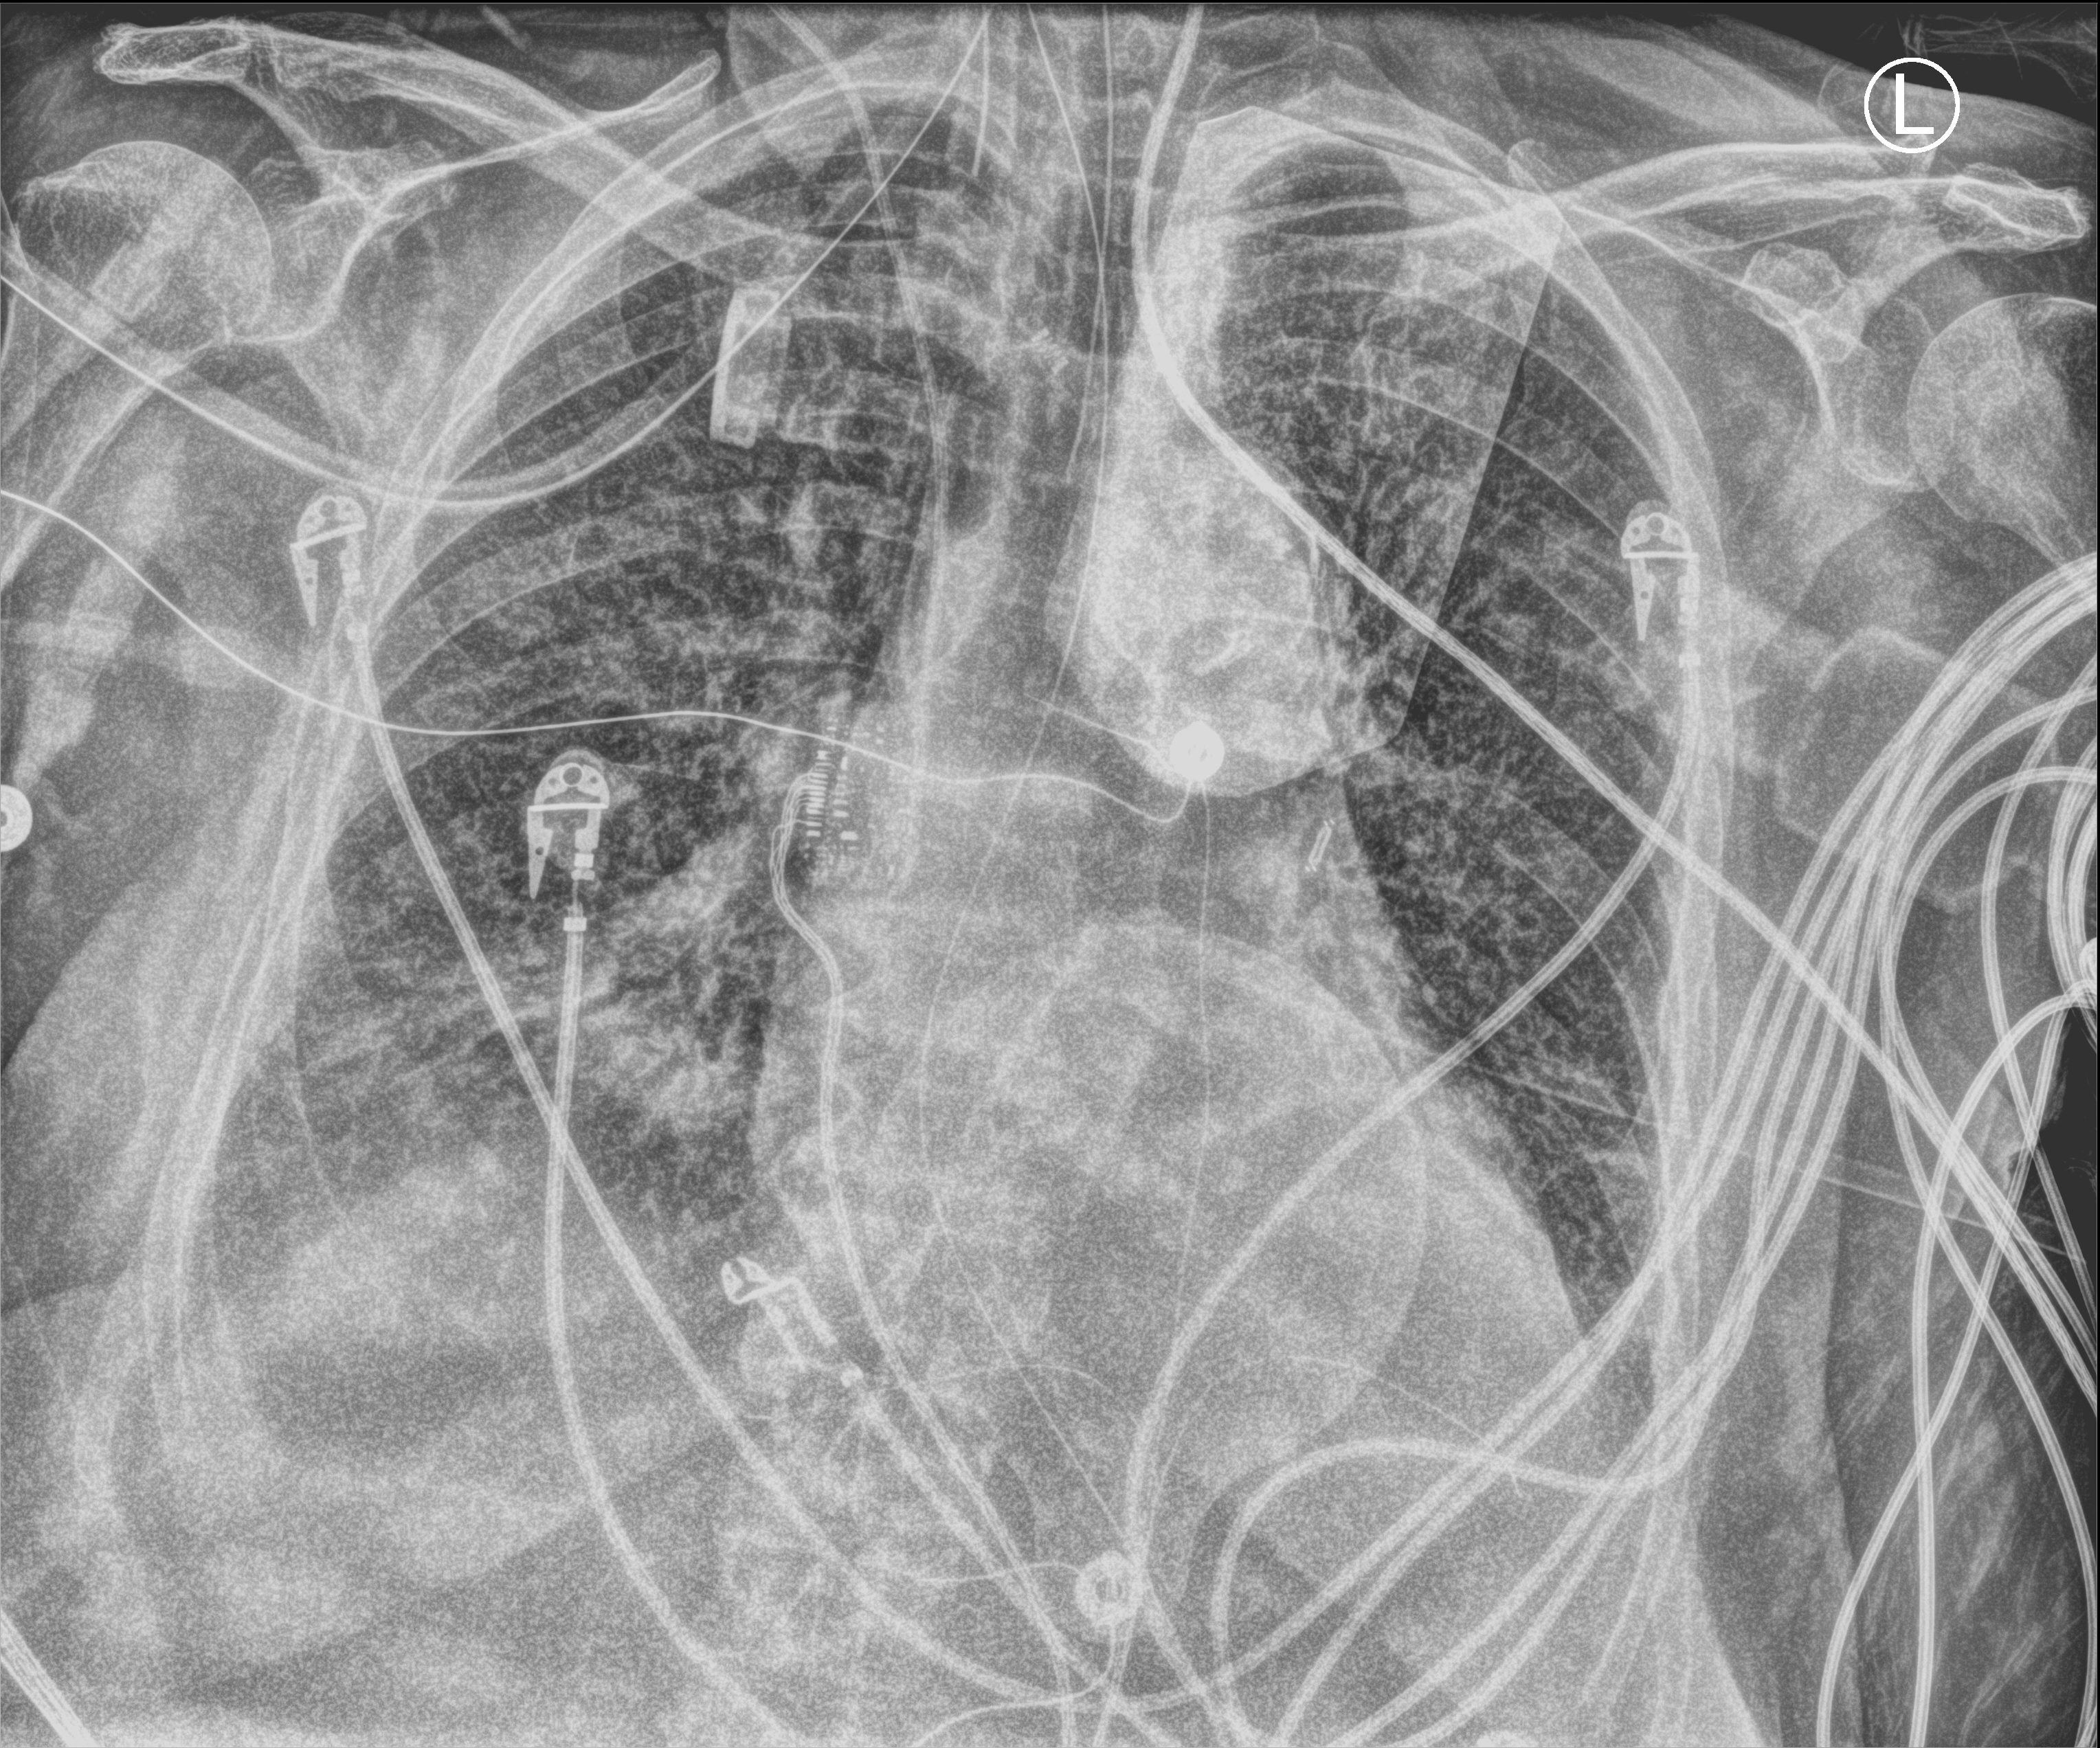
Chest X-ray (portable); anteroposterior (AP) projection. Patient hospitalised with COVID-19; female, aged 75–90 years.
From the hospital-stay record, not from the radiograph (when in the stay this image was taken is not recorded): admitted to intensive care during this hospital stay: yes; length of hospital stay: 10 days.